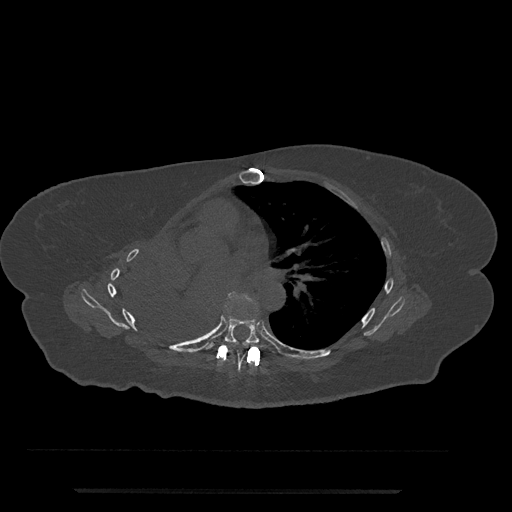
CT including the spine, one axial slice; slice 466 of 797 in the series (ordered by position); 120 kVp; bone window (W 1800 / L 400 HU); 0.5 mm slice thickness; 512 × 512 image matrix. Patient: female, 51 years. Case-level facts recorded for this patient, not image findings: primary cancer: neuro.
Outlined on this slice (semi-automatic segmentation, software-assisted and operator-edited):
- T6 vertebra: bounding box (x1, y1, x2, y2) in pixels: (224, 346, 246, 371)
- T7 vertebra: (215, 297, 276, 353)